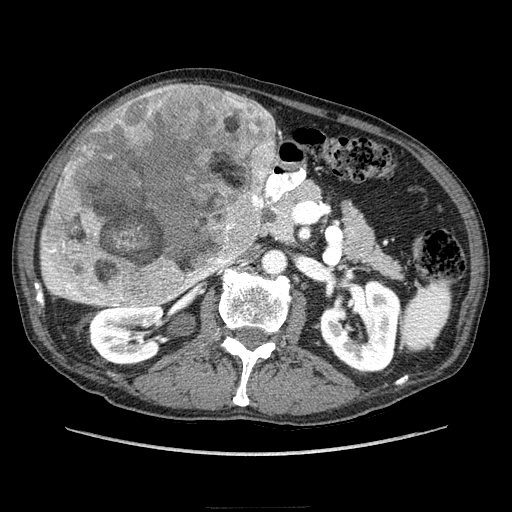
Contrast-enhanced abdominal CT (liver protocol), one axial slice; position 111 of 218 along the scan axis; reconstruction kernel STANDARD; soft-tissue window (W 400 / L 40 HU); 2.5 mm slice thickness; 512 × 512 image matrix, field of view 380 × 380 mm. From the clinical record (not read from this slice): diagnosis: hepatocellular carcinoma (patient treated with transarterial chemoembolisation; whether this scan precedes or follows treatment is not stated here); TNM stage (as recorded): Stage-IIIA; Child-Pugh class: A; tumour differentiation: well differentiated; tumour nodularity: multinodular.
Annotated regions visible in this slice (semi-automatic segmentation, software-assisted and operator-edited):
- liver parenchyma outside the tumour (the mass and vessels are separate outlines, so this box may not span the whole liver): bounding box <40,88,316,296> (left, top, right, bottom; pixels)
- mass: <43,83,276,309>
- liver vessels: <43,202,286,292>